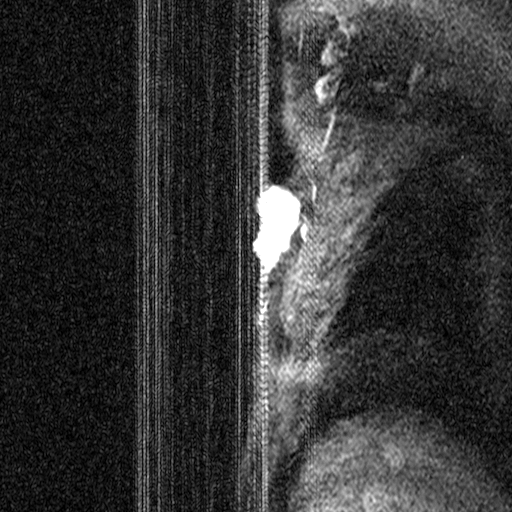
Breast MRI (dynamic contrast-enhanced), one sagittal slice; position 32 of 44 along the scan axis; dynamic contrast-enhanced study with each time point stored as its own series, time point 2 of 3 at this slice position (early post-contrast, ordered by acquisition time); 1.5 T; TE 4.5 ms, TR 11 ms; 3 mm slice thickness; 512 × 512 image matrix. Patient: female, 44 years. Case-level facts recorded for this patient, not image findings: setting: breast cancer imaged before/during neoadjuvant chemotherapy; receptor status: HR-positive, HER2-negative.
Annotated regions visible in this slice (semi-automatically segmented with operator editing):
- analysis volume of interest (the breast-tissue region the enhancement analysis was run in; not a lesion): box from (x=206, y=164) to (x=319, y=299) px
- tumour enhancement mask (voxels above the 90 % enhancement threshold inside the analysis volume of interest): (x=253, y=164)–(x=314, y=266)